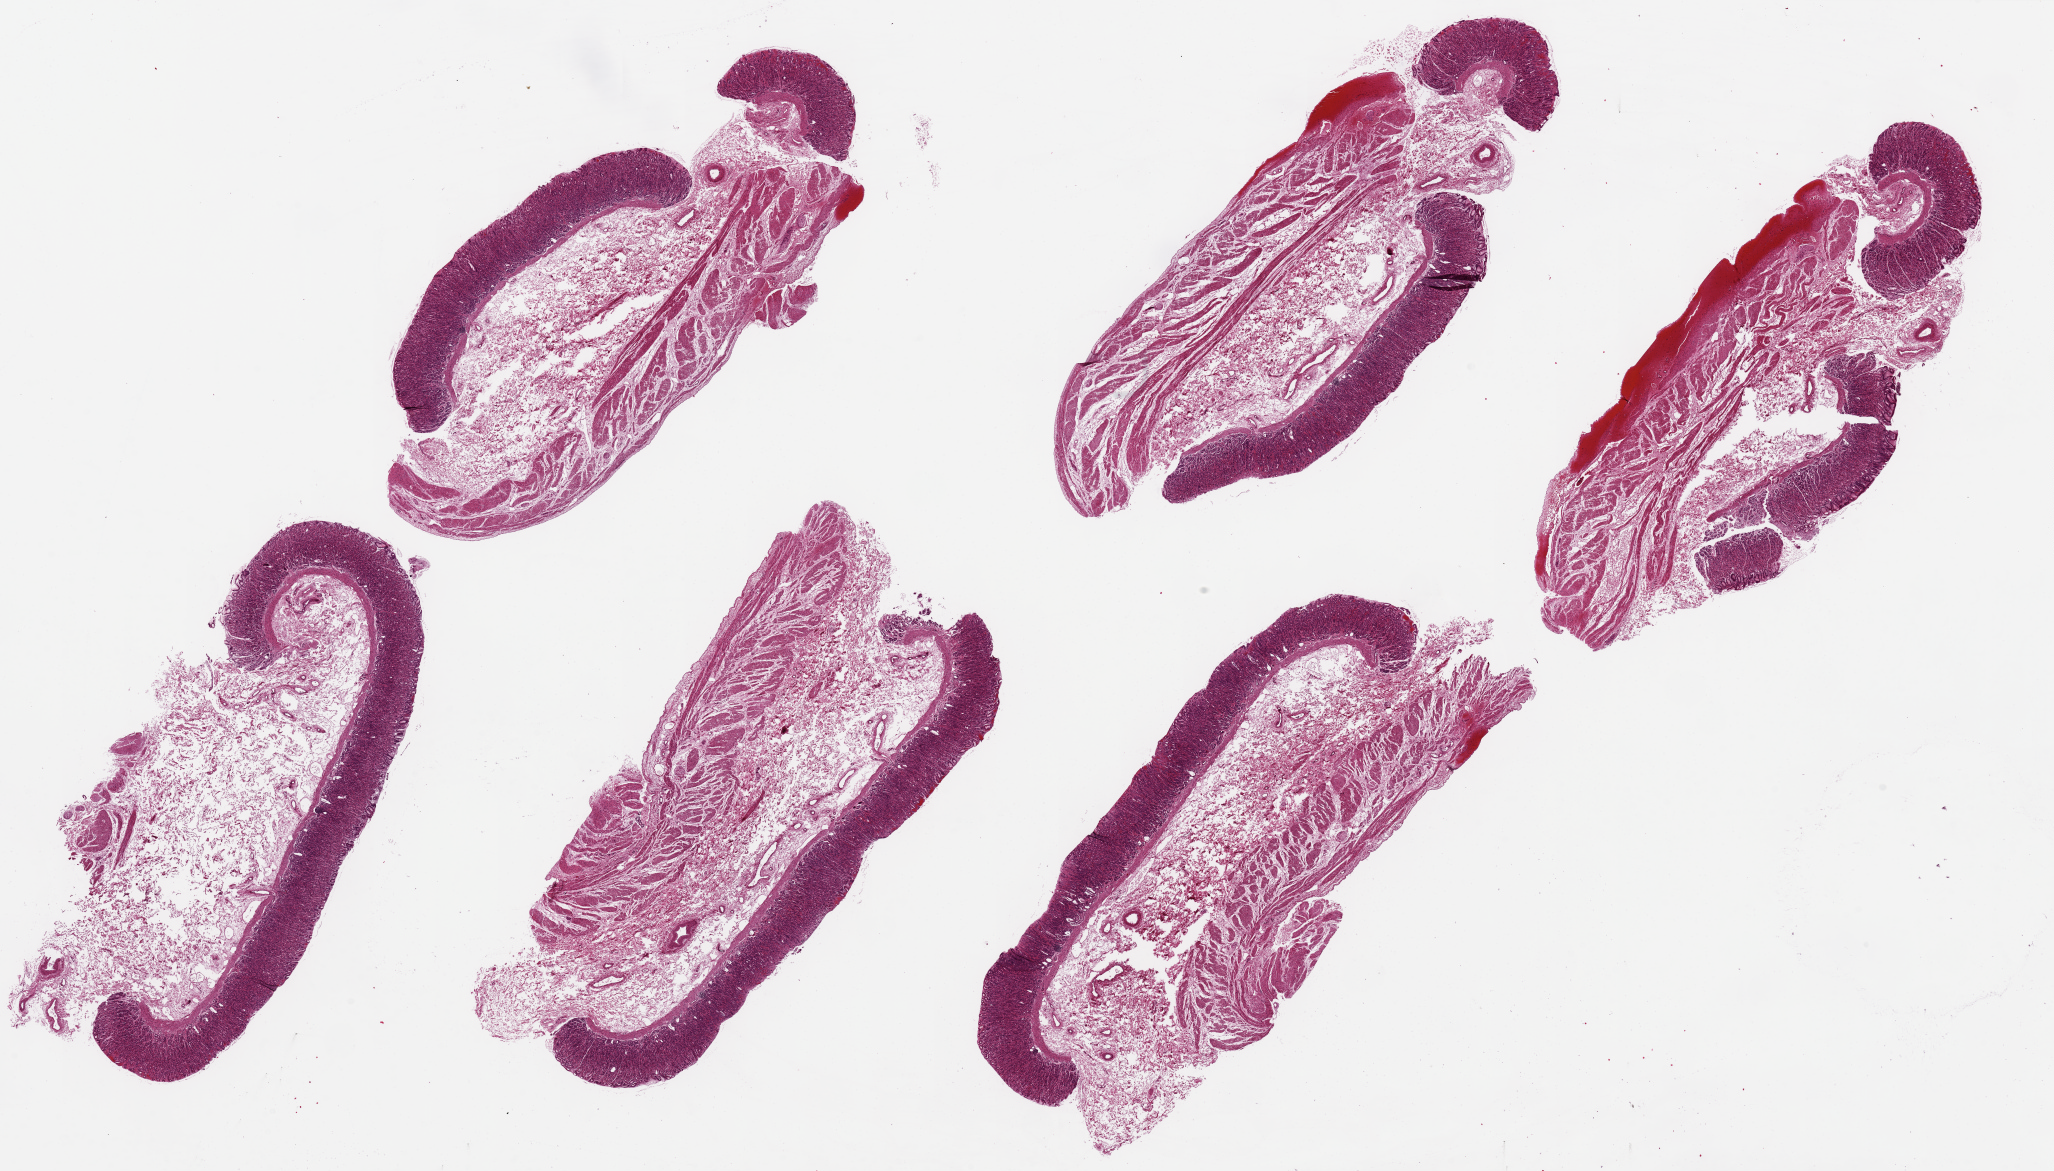
Digitized hematoxylin and eosin (H&E)-stained section, brightfield — a low-resolution overview of the entire scanned area, about 32.5 x 18.5 mm (slide scanned at 20x), PAXgene-fixed, paraffin-embedded tissue, section of stomach (target tissue), tissue donor sample. Donor sex: female.
Review note (as recorded): 6 pieces, ~9x4mm. Mucosa extremely well preserved, ~25% of thickness.